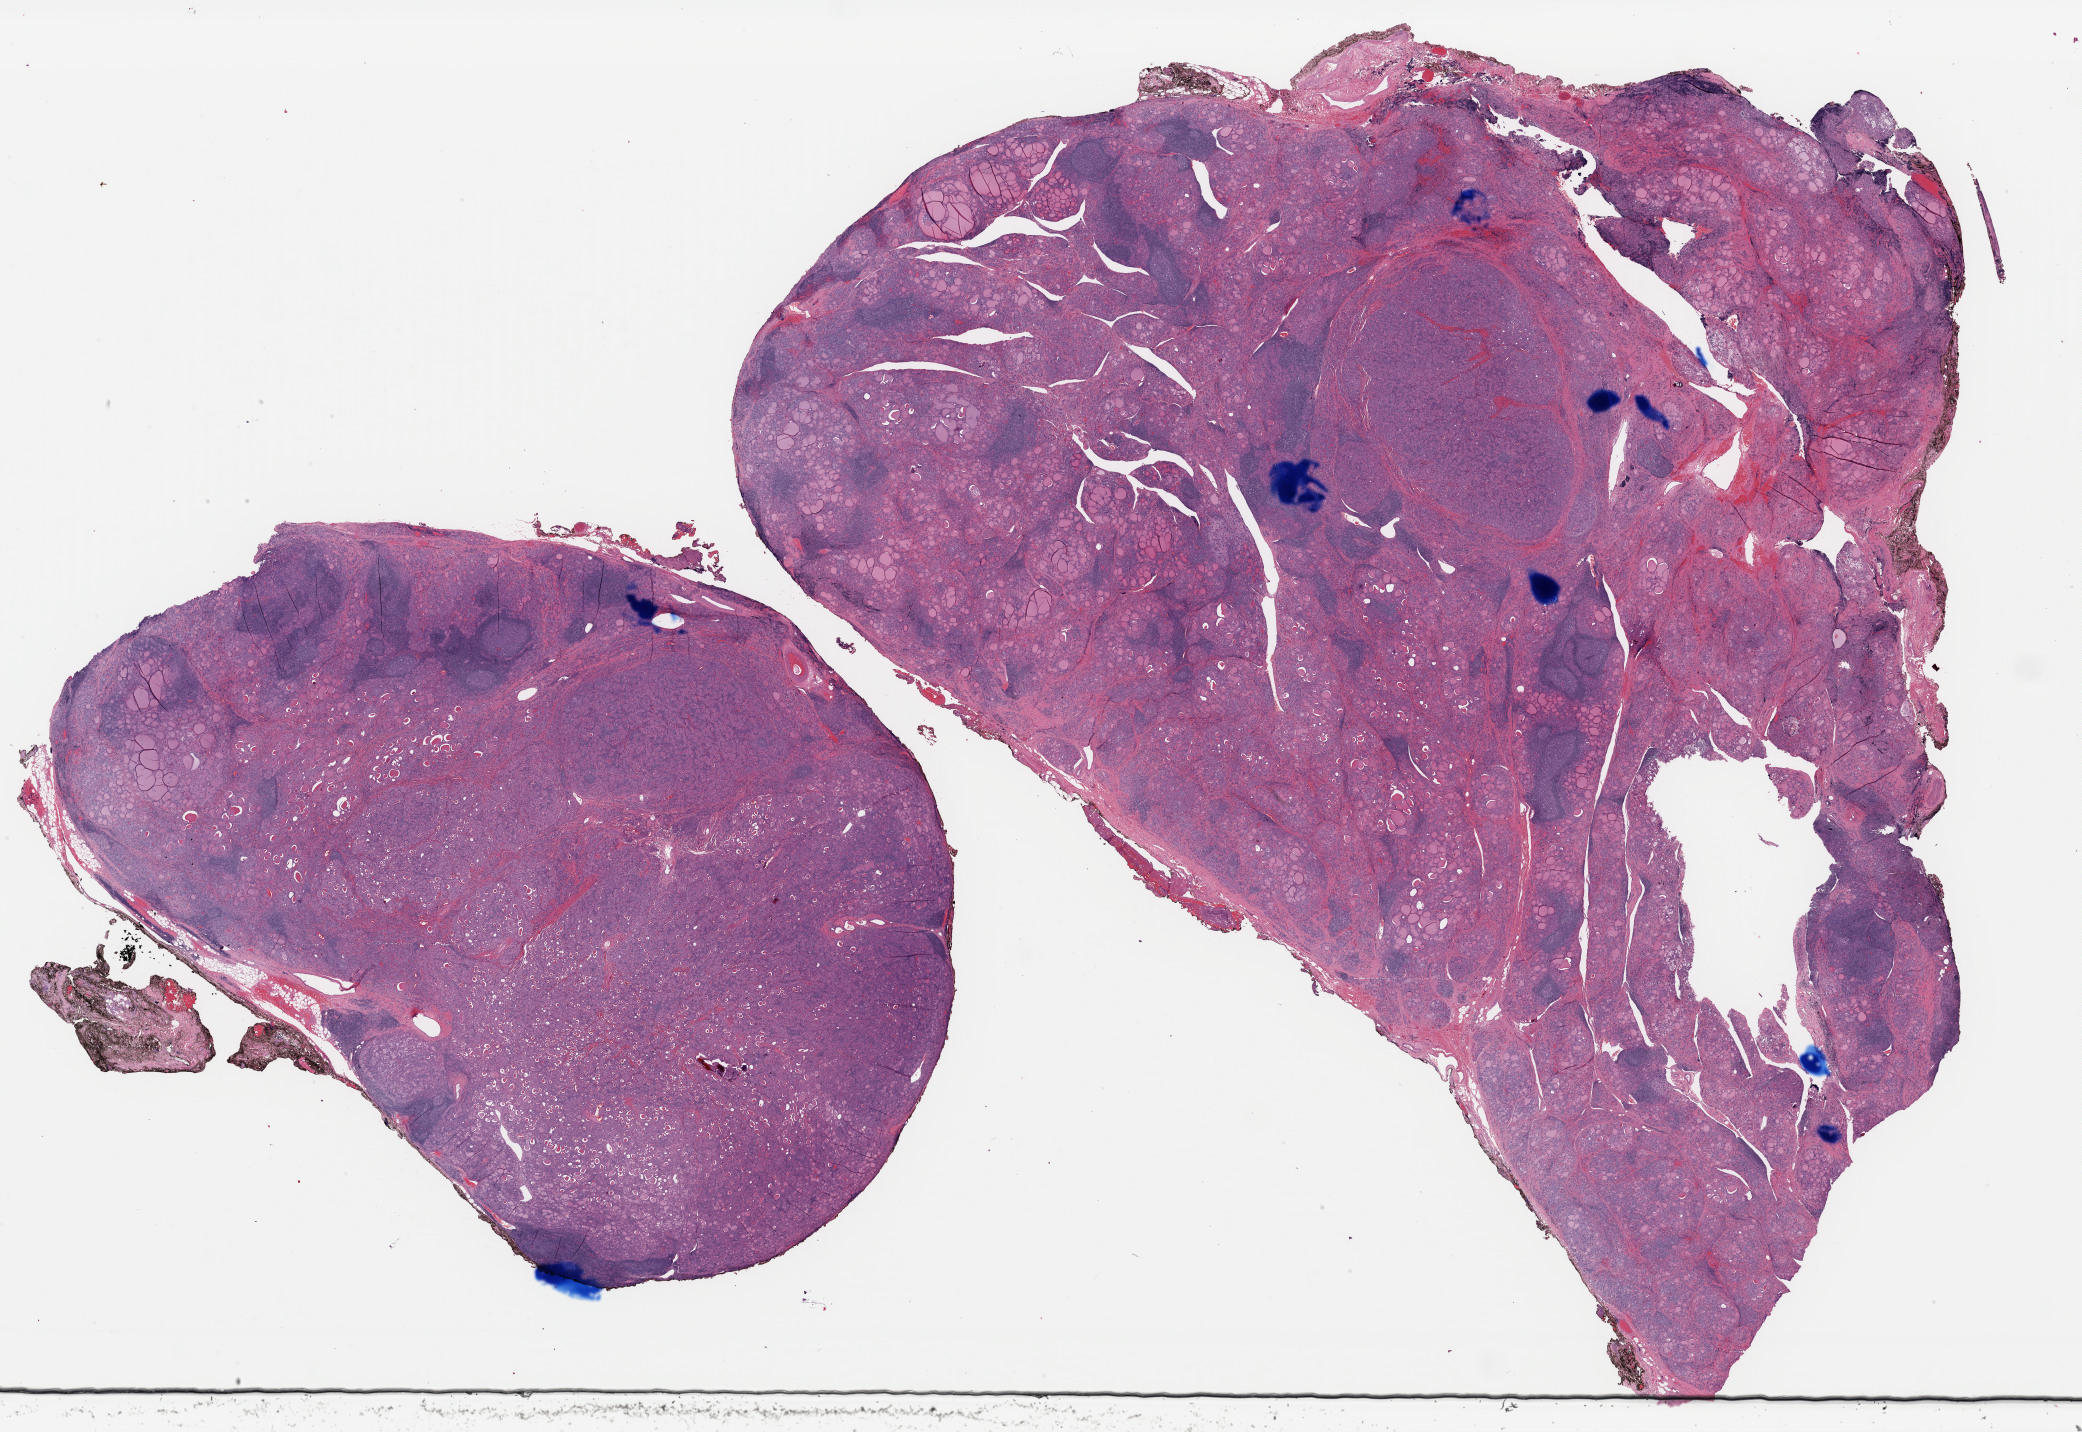
Whole-slide histology image, H&E-stained — whole scanned area (about 32.9 x 22.6 mm, acquisition: 40x scan) shown as a low-resolution overview, formalin-fixed paraffin-embedded (FFPE) diagnostic section, thyroid, primary tumour sample. Female, age 46 years at initial diagnosis.
Histologic diagnosis: Papillary adenocarcinoma, NOS (thyroid gland).